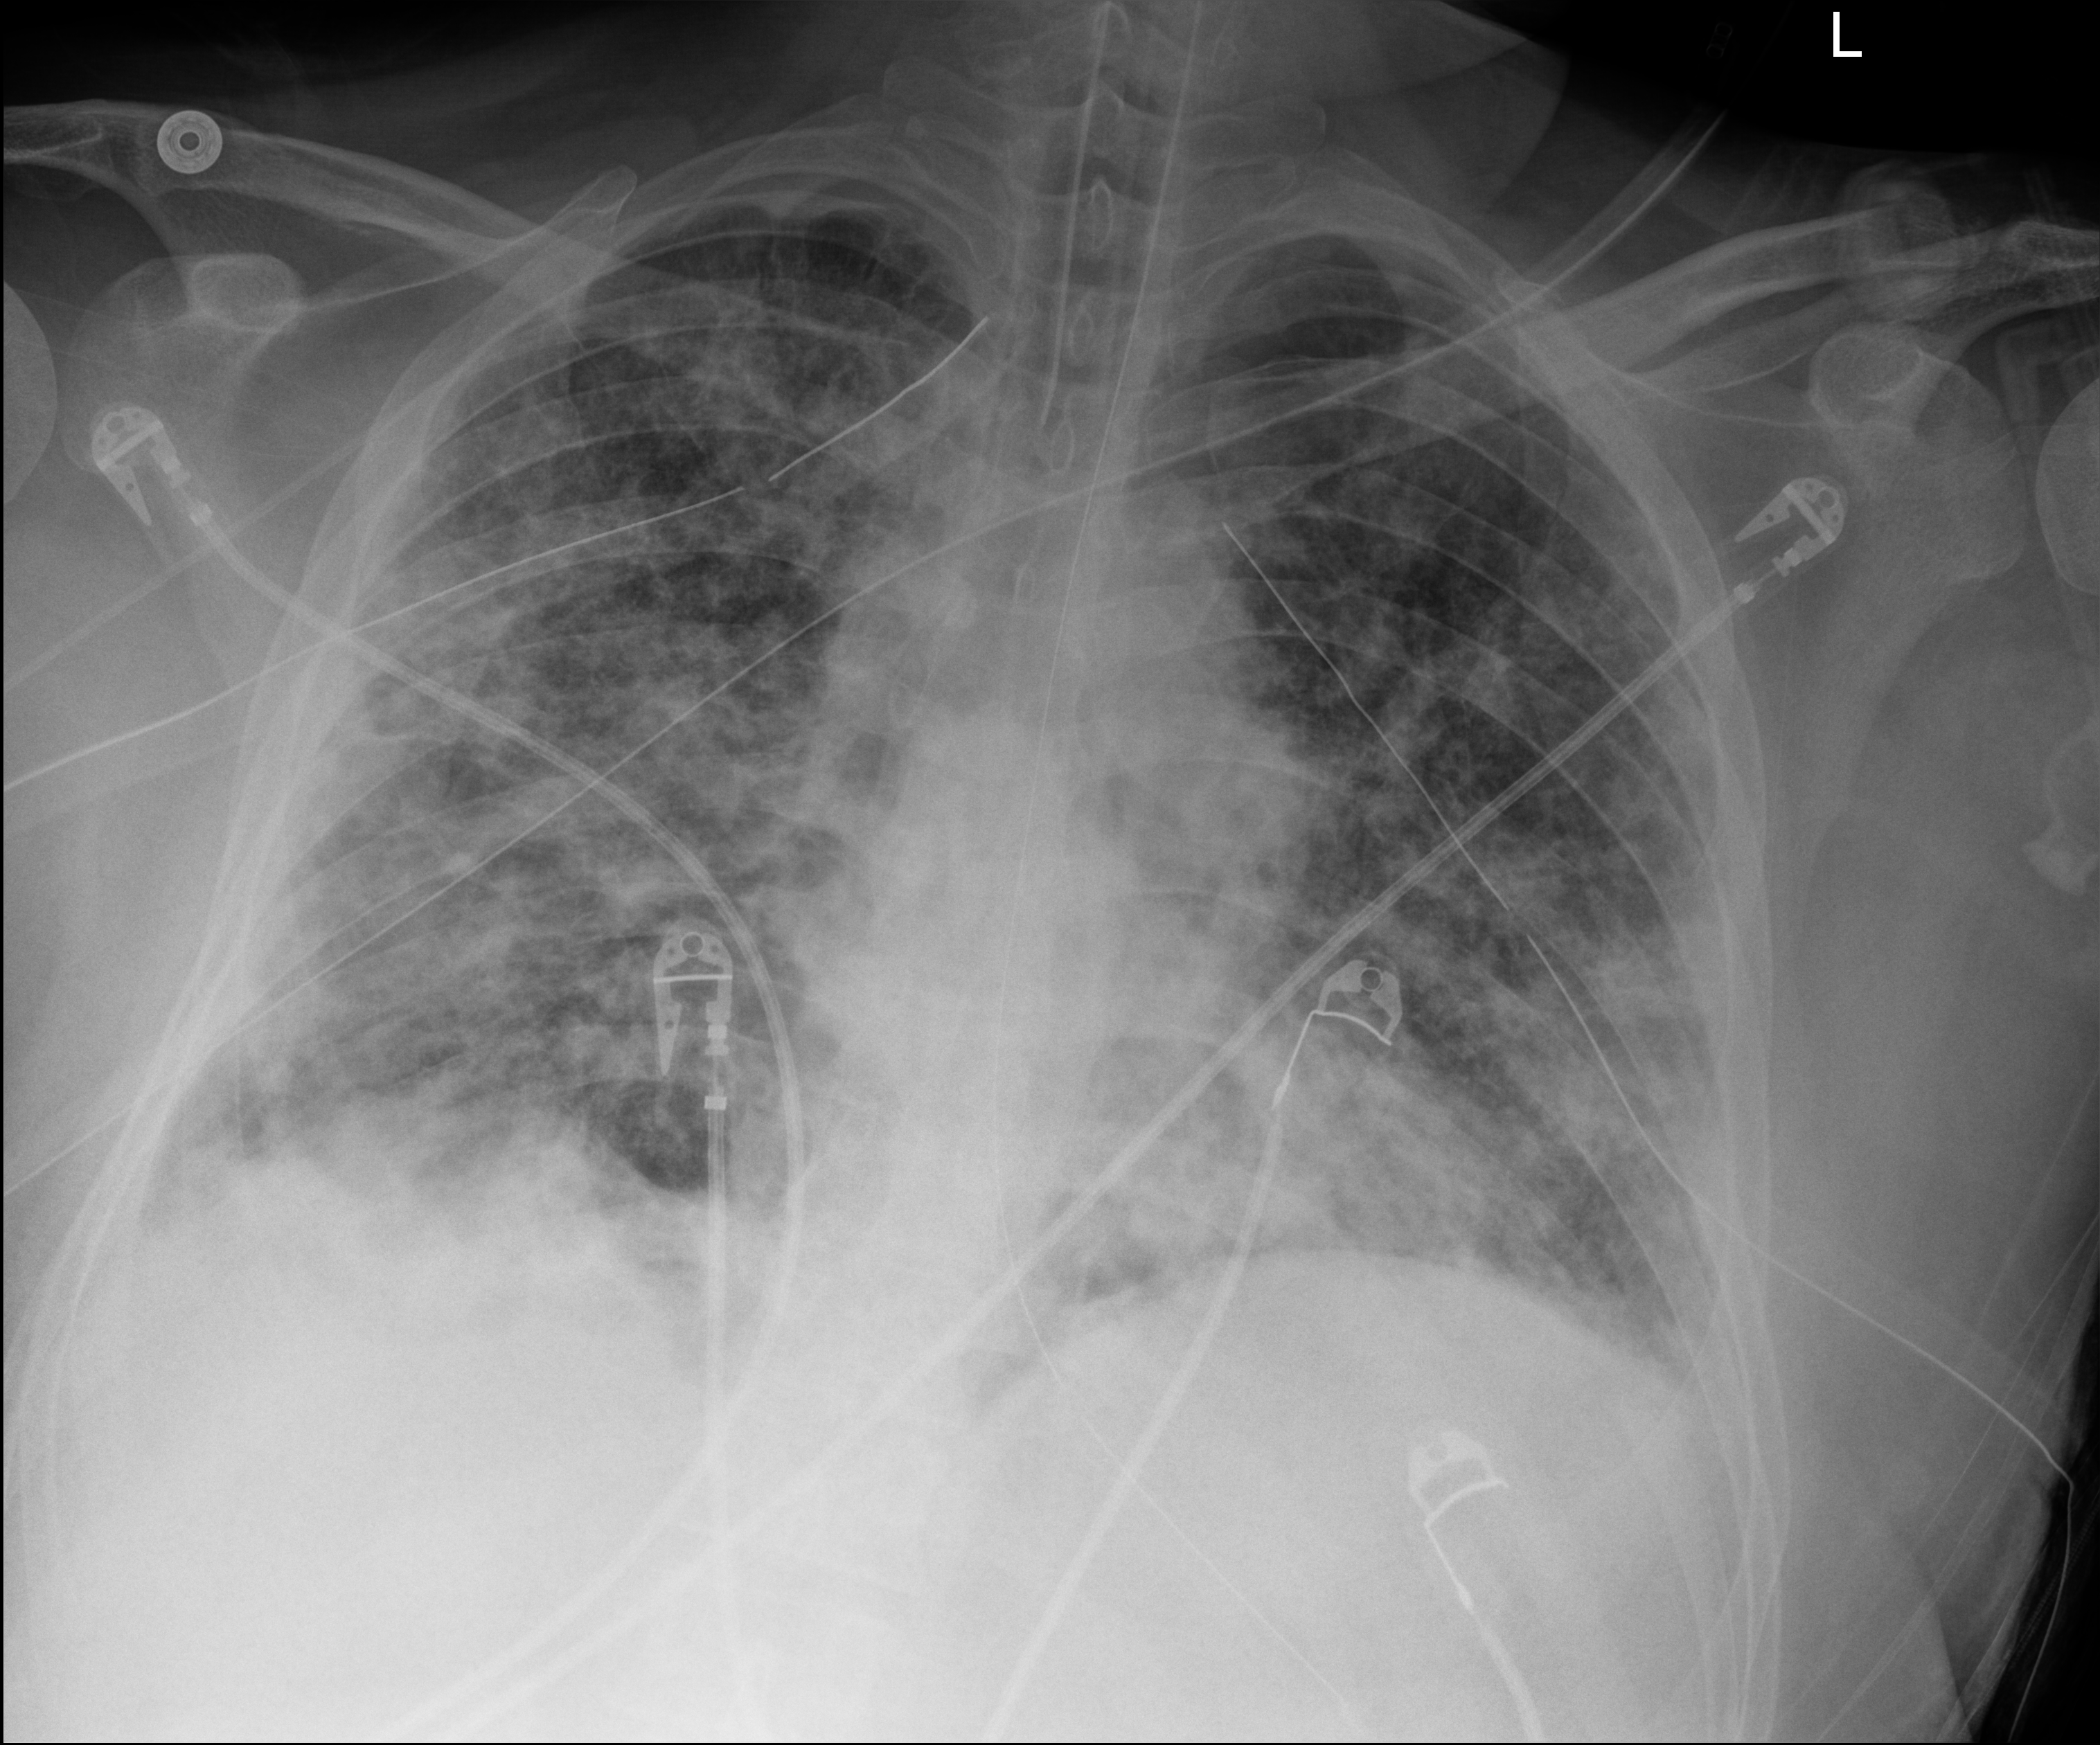
Portable chest radiograph, anteroposterior (AP) projection. Patient hospitalised with COVID-19; male, aged 18–59 years.
Hospital-stay facts (about this admission, not read from this image; timing relative to this image not recorded):
- diabetes (admission record): yes
- other chronic lung disease (admission record): no